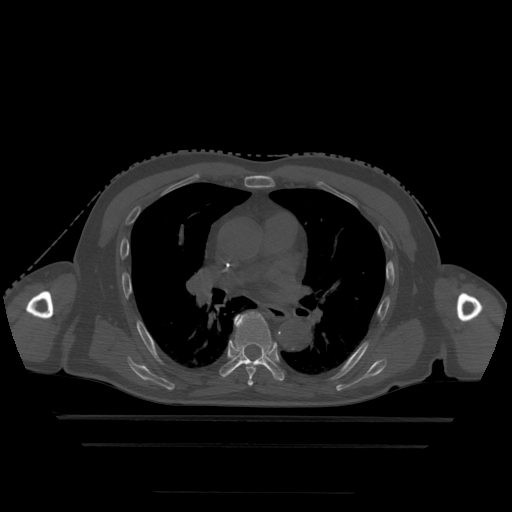
CT including the spine, one axial slice; bone window (W 1800 / L 400 HU); 1.25 mm slice thickness; 512 × 512 image matrix. Patient age 68 years. From the clinical record (not read from this slice): primary cancer: urothelial.
Outlined on this slice (semi-automatically segmented with operator editing):
- T5 vertebra: bounding box [x1, y1, x2, y2] px = [248, 379, 254, 387]
- T6 vertebra: [247, 366, 256, 379]
- T7 vertebra: [220, 313, 285, 382]